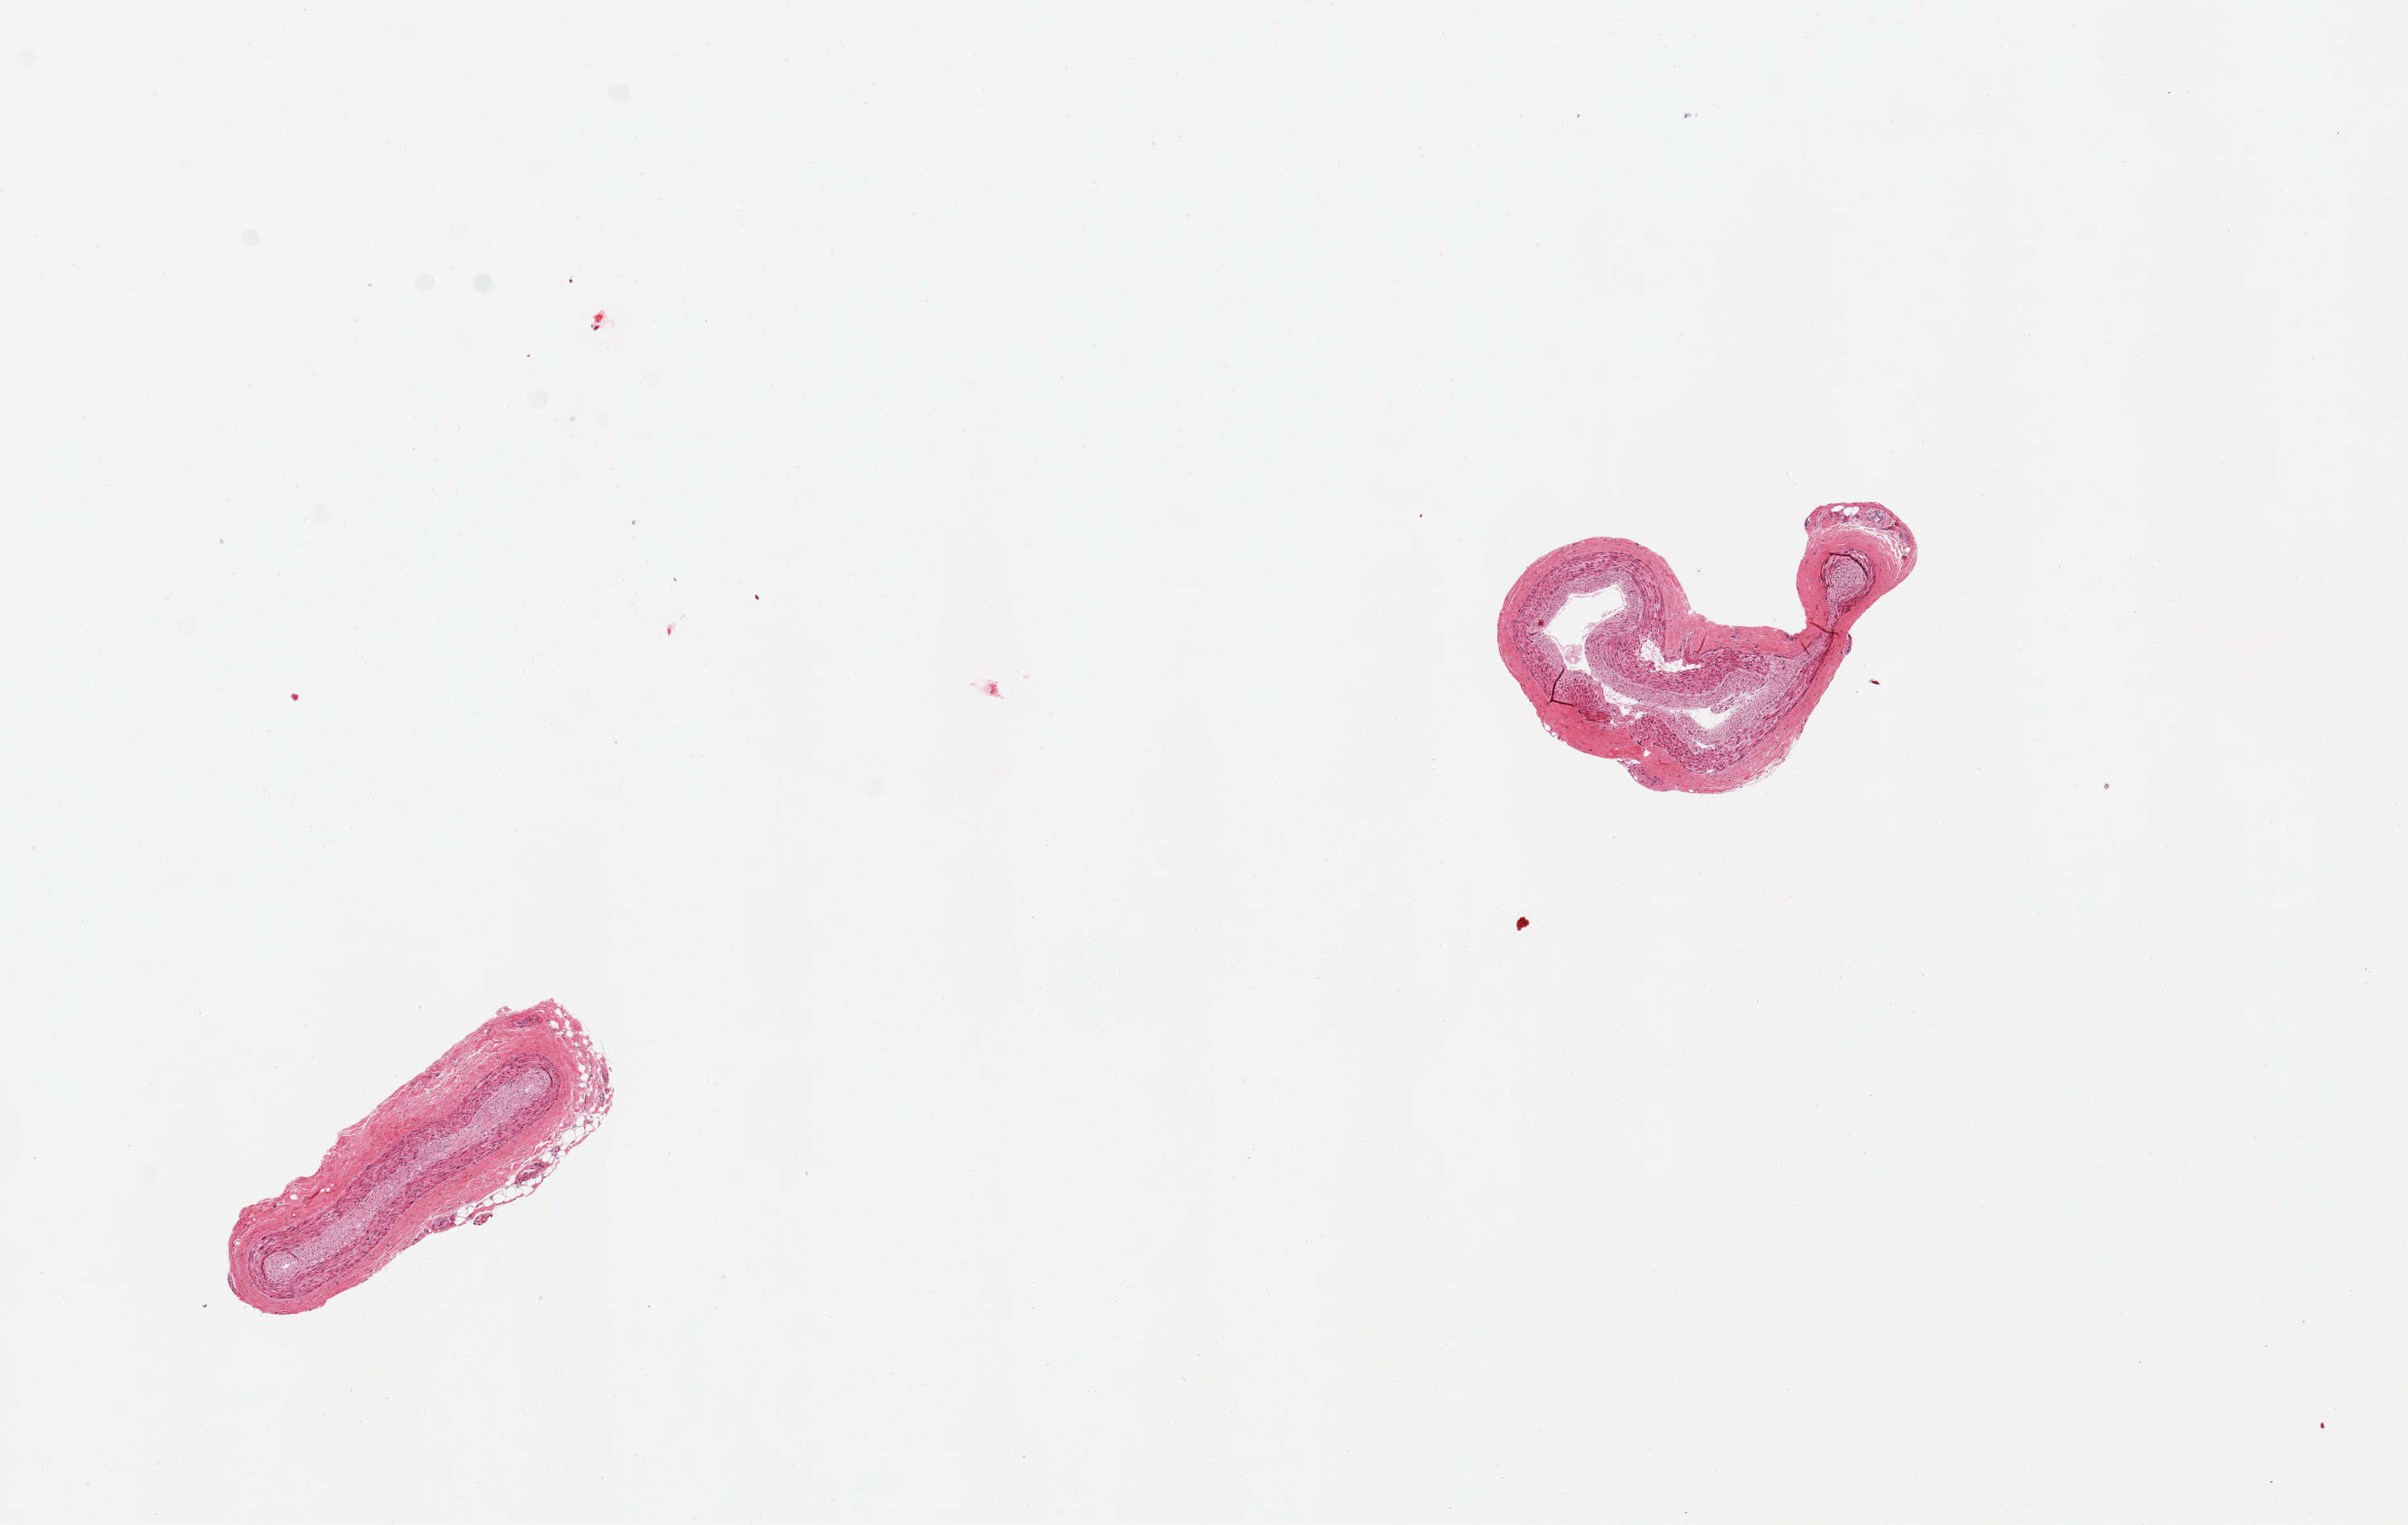
Digitized haematoxylin and eosin-stained section, low-resolution overview of the scanned area, about 11.8 x 7.5 mm (acquisition: 20x scan), PAXgene-fixed paraffin-embedded (PFPE) section, sampled site (target tissue): coronary artery, donor tissue sample. Female donor.
Pathologist's review note for this sample: 2 pieces, clean specimens, minimal atherosis.